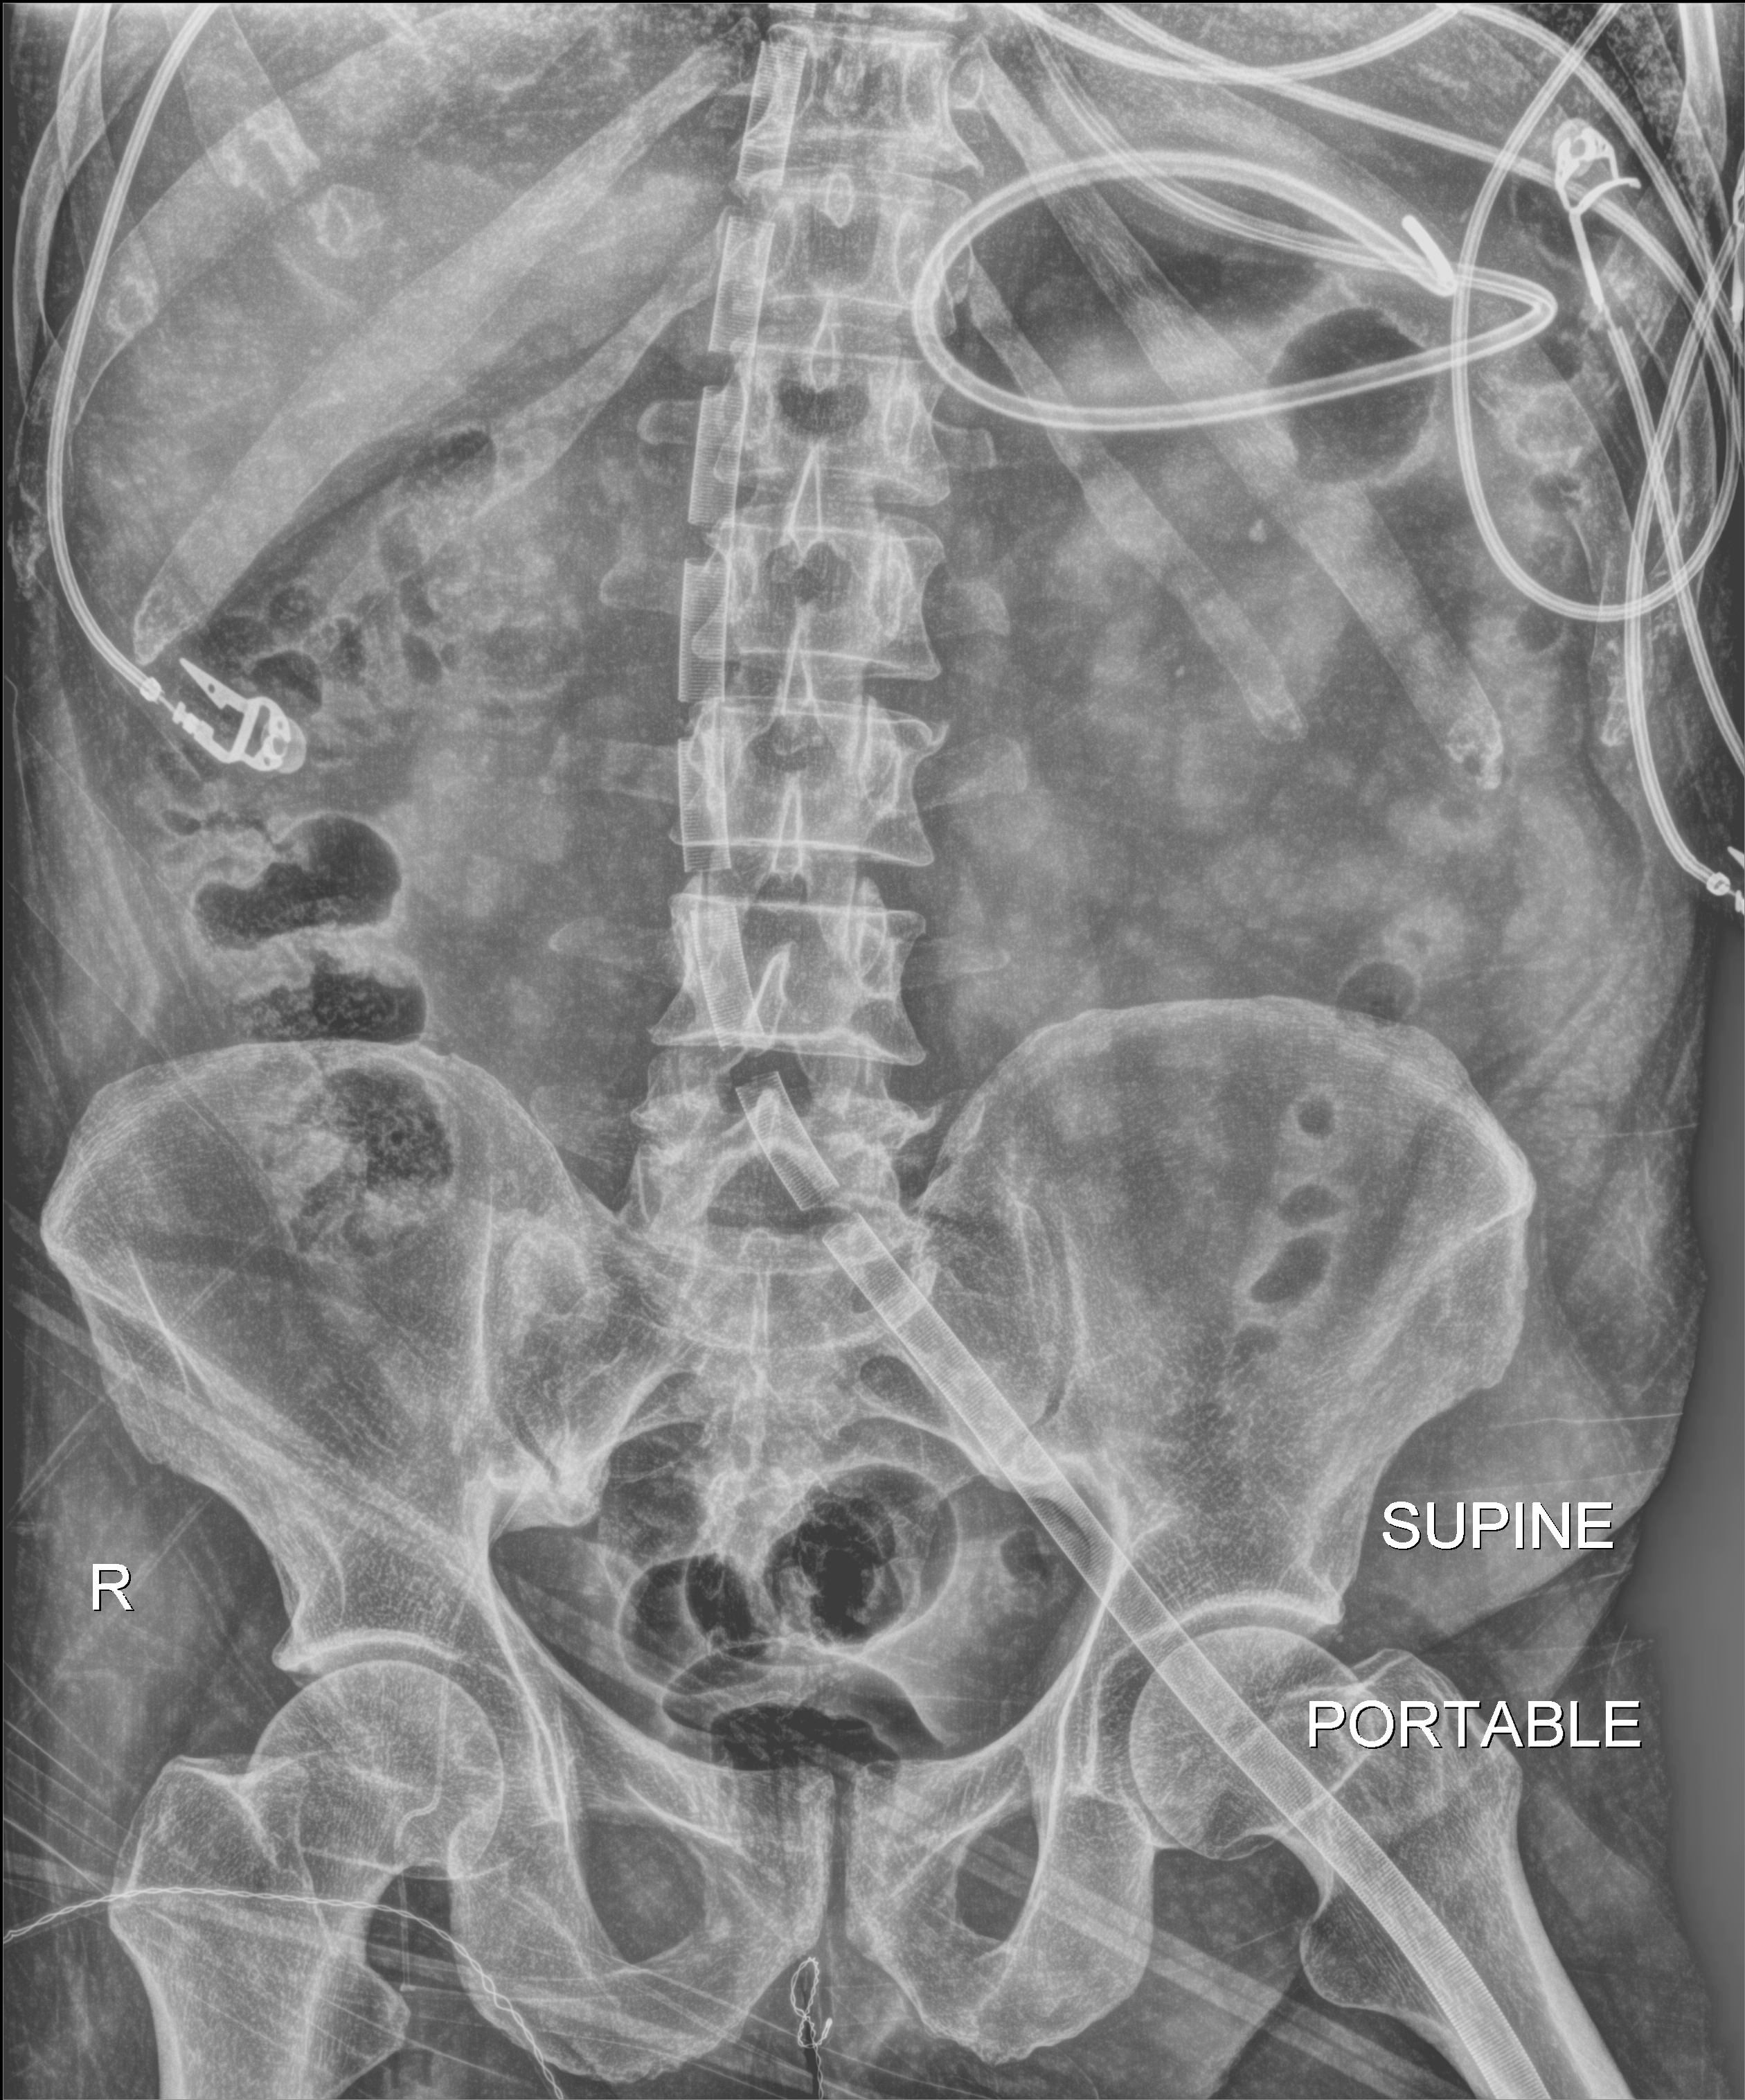
Abdomen radiograph. Male patient hospitalised with COVID-19, age 18–59 years.
Admission-level facts for this patient (not findings on this image; timing relative to this image not recorded):
- mechanically ventilated during this hospital stay: yes